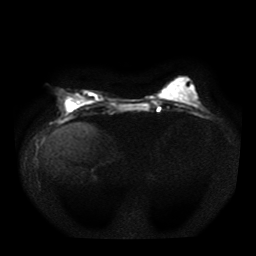
Breast MRI, one axial slice. Position 15 of 41 along the scan axis. Diffusion-weighted series; image 2 of 4 stored at this slice position (different b-values; order by instance number). 1.5 T. 5 mm slice thickness. 256 × 256 image matrix, field of view 330 × 330 mm. Female patient.
Structures marked on this image (expert manual segmentation):
- tumour on diffusion-weighted imaging: bounding box [x1, y1, x2, y2] px = [67, 102, 77, 111]